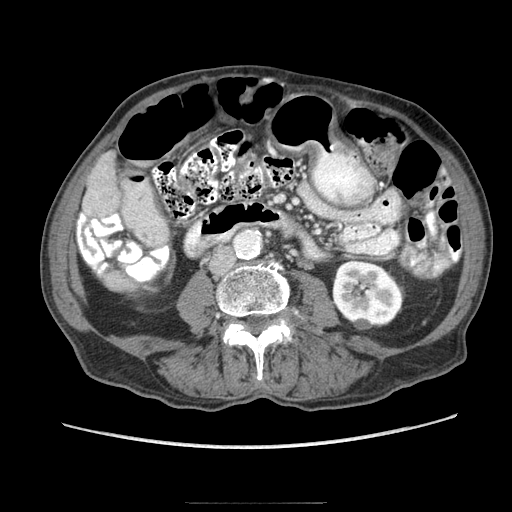
Contrast-enhanced abdominal CT (liver protocol), one axial slice; slice 12 of 83 in the series (ordered by position); reconstruction kernel STANDARD; 140 kVp; soft-tissue window (W 400 / L 40 HU); 2.5 mm slice thickness; 512 × 512 image matrix, field of view 360 × 360 mm. From the clinical record (not read from this slice): diagnosis: hepatocellular carcinoma (patient treated with transarterial chemoembolisation; whether this scan precedes or follows treatment is not stated here); TNM stage (as recorded): Stage-I; Child-Pugh class: A; tumour differentiation: moderately differentiated; tumour nodularity: uninodular.
Outlined on this slice (semi-automatically segmented with operator editing):
- liver parenchyma outside the tumour (the mass and vessels are separate outlines, so this box may not span the whole liver): bounding box (x1, y1, x2, y2) in pixels: (82, 152, 119, 221)
- liver vessels: (80, 214, 86, 220)